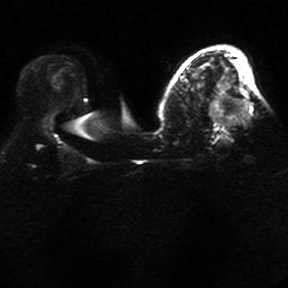
Breast MRI, one axial slice. Slice 17 of 34 in the series (ordered by position). Diffusion-weighted series; image 2 of 4 stored at this slice position (different b-values; order by instance number). 1.5 T. 5 mm slice thickness. 288 × 288 image matrix, field of view 340 × 340 mm. Female patient.
Annotated regions visible in this slice (expert manual segmentation):
- tumour on diffusion-weighted imaging: bounding box <208,86,248,125> (left, top, right, bottom; pixels)